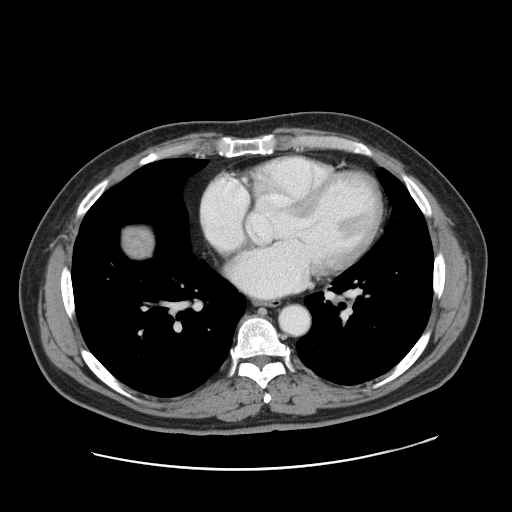
Contrast-enhanced abdominal CT, one axial slice; slice 170 of 178 in the series (ordered by position); 120 kVp; intravenous contrast given; soft-tissue window (W 400 / L 40 HU); 512 × 512 image matrix, field of view 403 × 403 mm. Male patient, age 63 years. Case-level facts recorded for this patient, not image findings: diagnosis: colorectal cancer liver metastases, imaged before liver resection; multiple liver metastases: yes; largest metastasis: 8 cm; chemotherapy before resection: no.
Annotated regions visible in this slice (outlined manually by an expert reader):
- liver: box from (x=123, y=227) to (x=153, y=257) px
- liver metastasis: (x=125, y=233)–(x=151, y=256)